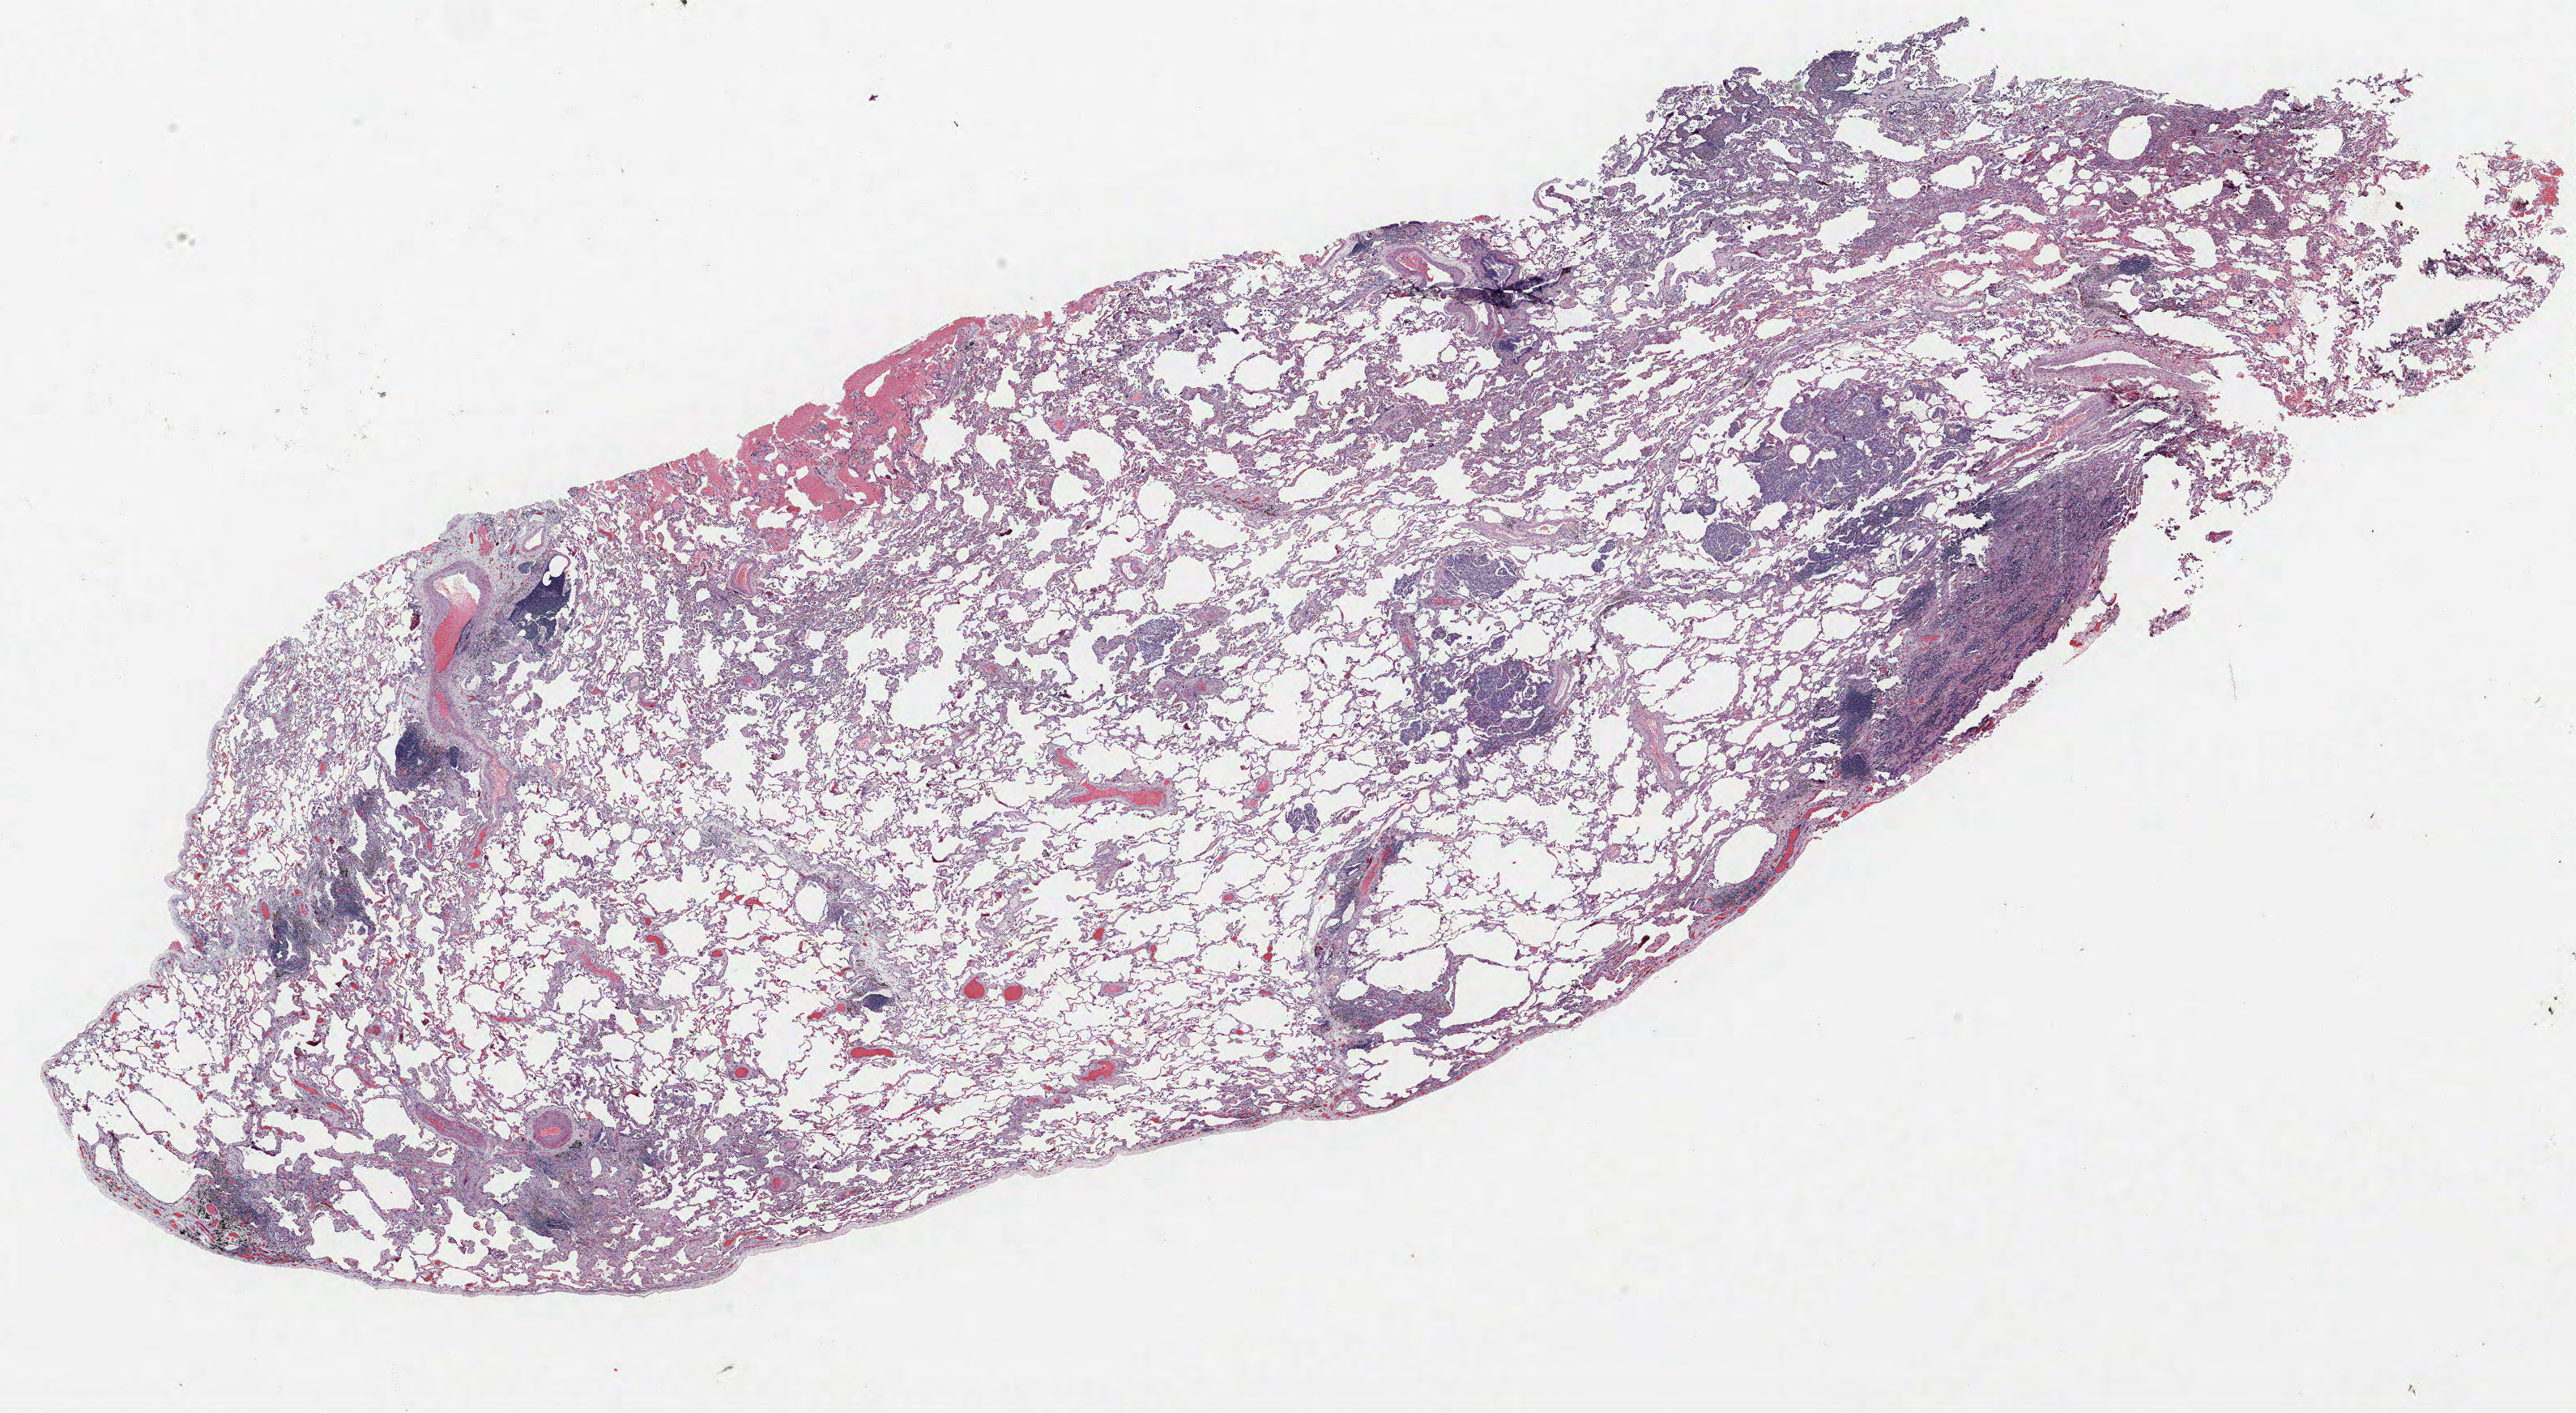
H&E whole-slide image — whole scanned area (about 25.4 x 14.0 mm) shown as a low-resolution overview. FFPE section. Lung. Female patient, aged 62 at enrolment.
Participant's lung-cancer diagnosis: Adenocarcinoma, NOS.